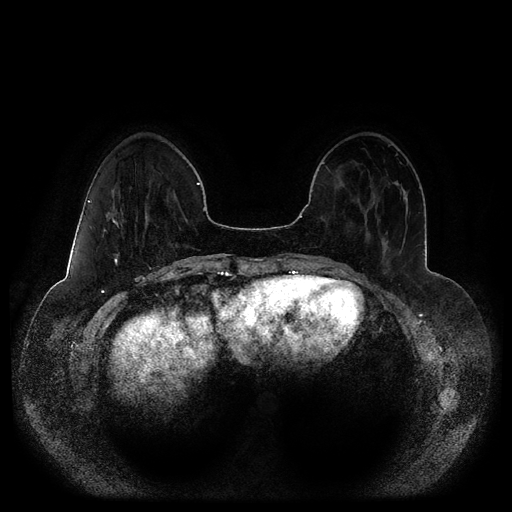
Breast MRI (dynamic contrast-enhanced, multi-phase), one axial slice. Position 32 of 116 along the scan axis. Dynamic contrast-enhanced series, time point 2 of 5 at this slice position (early post-contrast). 1.5 T. TE 2.5 ms, TR 5.2 ms. 2 mm slice thickness. 512 × 512 image matrix, field of view 390 × 390 mm. Female patient, age 44 years.
Structures marked on this image (semi-automatic segmentation, software-assisted and operator-edited):
- breast lesion (labelled 'tumour' in the annotation; benign lesions carry a separate 'benign' label): bounding box [x1, y1, x2, y2] px = [102, 189, 123, 266]